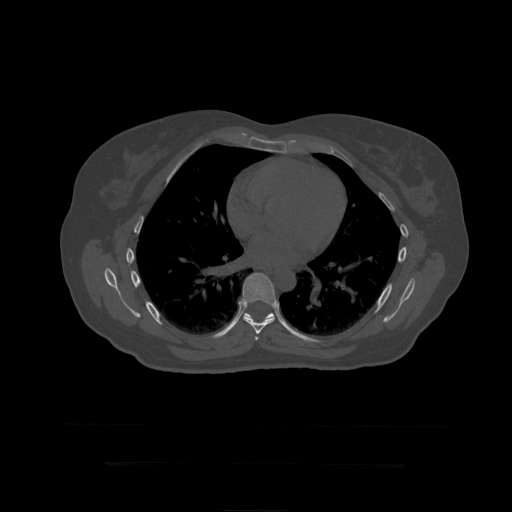
CT including the spine, one axial slice; slice 276 of 399 in the series (ordered by position); reconstruction kernel STANDARD; 120 kVp; bone window (W 1800 / L 400 HU); 1.25 mm slice thickness; 512 × 512 image matrix, field of view 450 × 450 mm. Patient age 41 years. From the clinical record (not read from this slice): primary cancer: breast.
Structures marked on this image (semi-automatic segmentation, software-assisted and operator-edited):
- T7 vertebra: bounding box (x1, y1, x2, y2) in pixels: (255, 336, 259, 341)
- T8 vertebra: (242, 273, 276, 334)
- T9 vertebra: (245, 291, 292, 334)